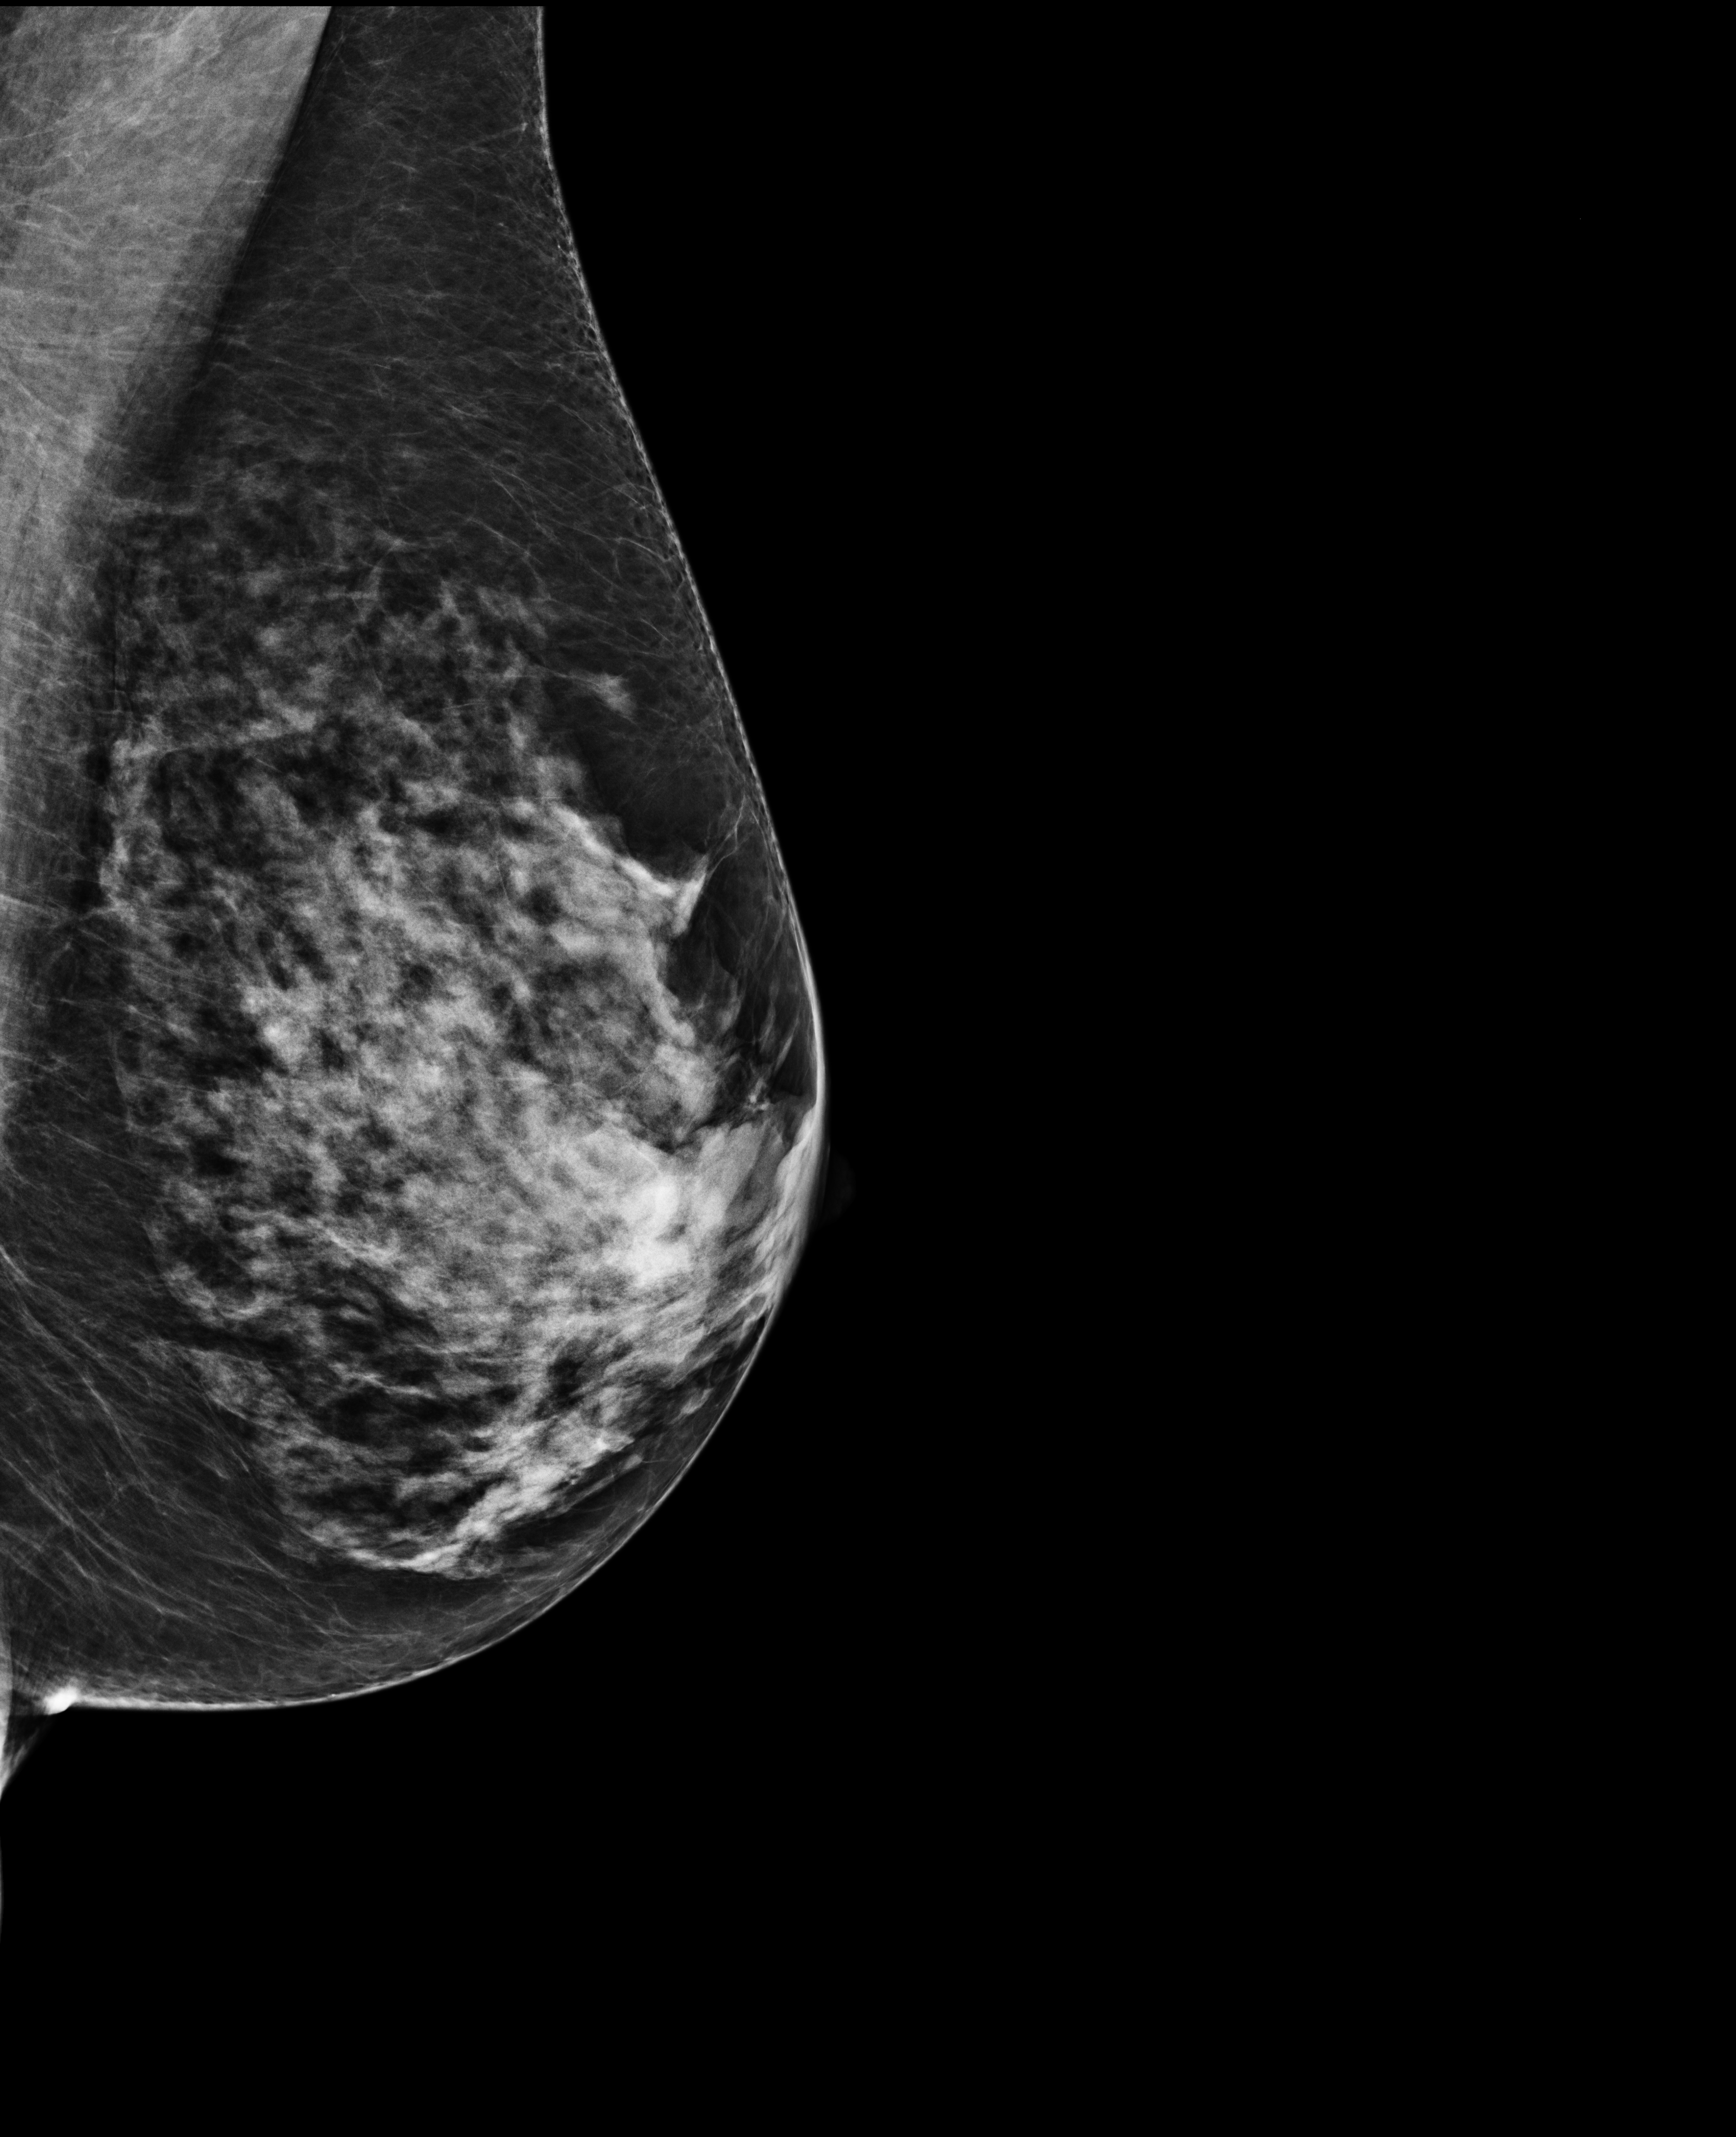
Digital mammogram (FFDM), left breast, MLO view, annual screening mammography examination. Female patient, age 66 years.
BI-RADS breast density category at the screening exam (both breasts, scale 1–4): 3. Final BI-RADS assessment for this screening round (tomosynthesis exam, both breasts): category 1. Recall: no recall after this screen.